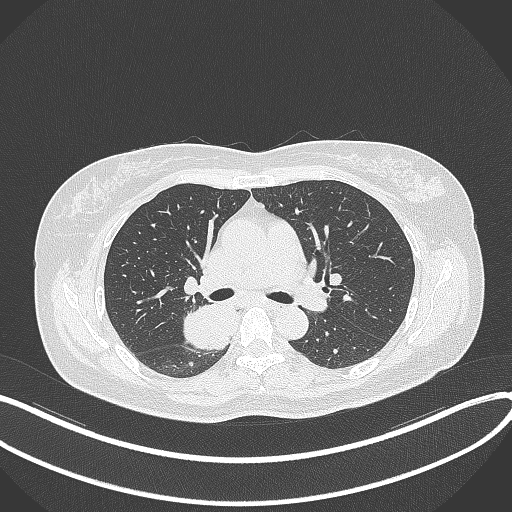
Chest CT, one axial slice; position 223 of 331 along the scan axis; reconstruction kernel B70f; lung window (W 1500 / L -600 HU); 1 mm slice thickness; 512 × 512 image matrix. Female patient, age 54 years. From the clinical record (not read from this slice): clinical TNM (as recorded): T4 N0 M0.
Annotated regions visible in this slice (bounding box drawn by a radiologist):
- lung tumour (recorded histology: adenocarcinoma): bounding box [x1, y1, x2, y2] px = [178, 301, 237, 357]